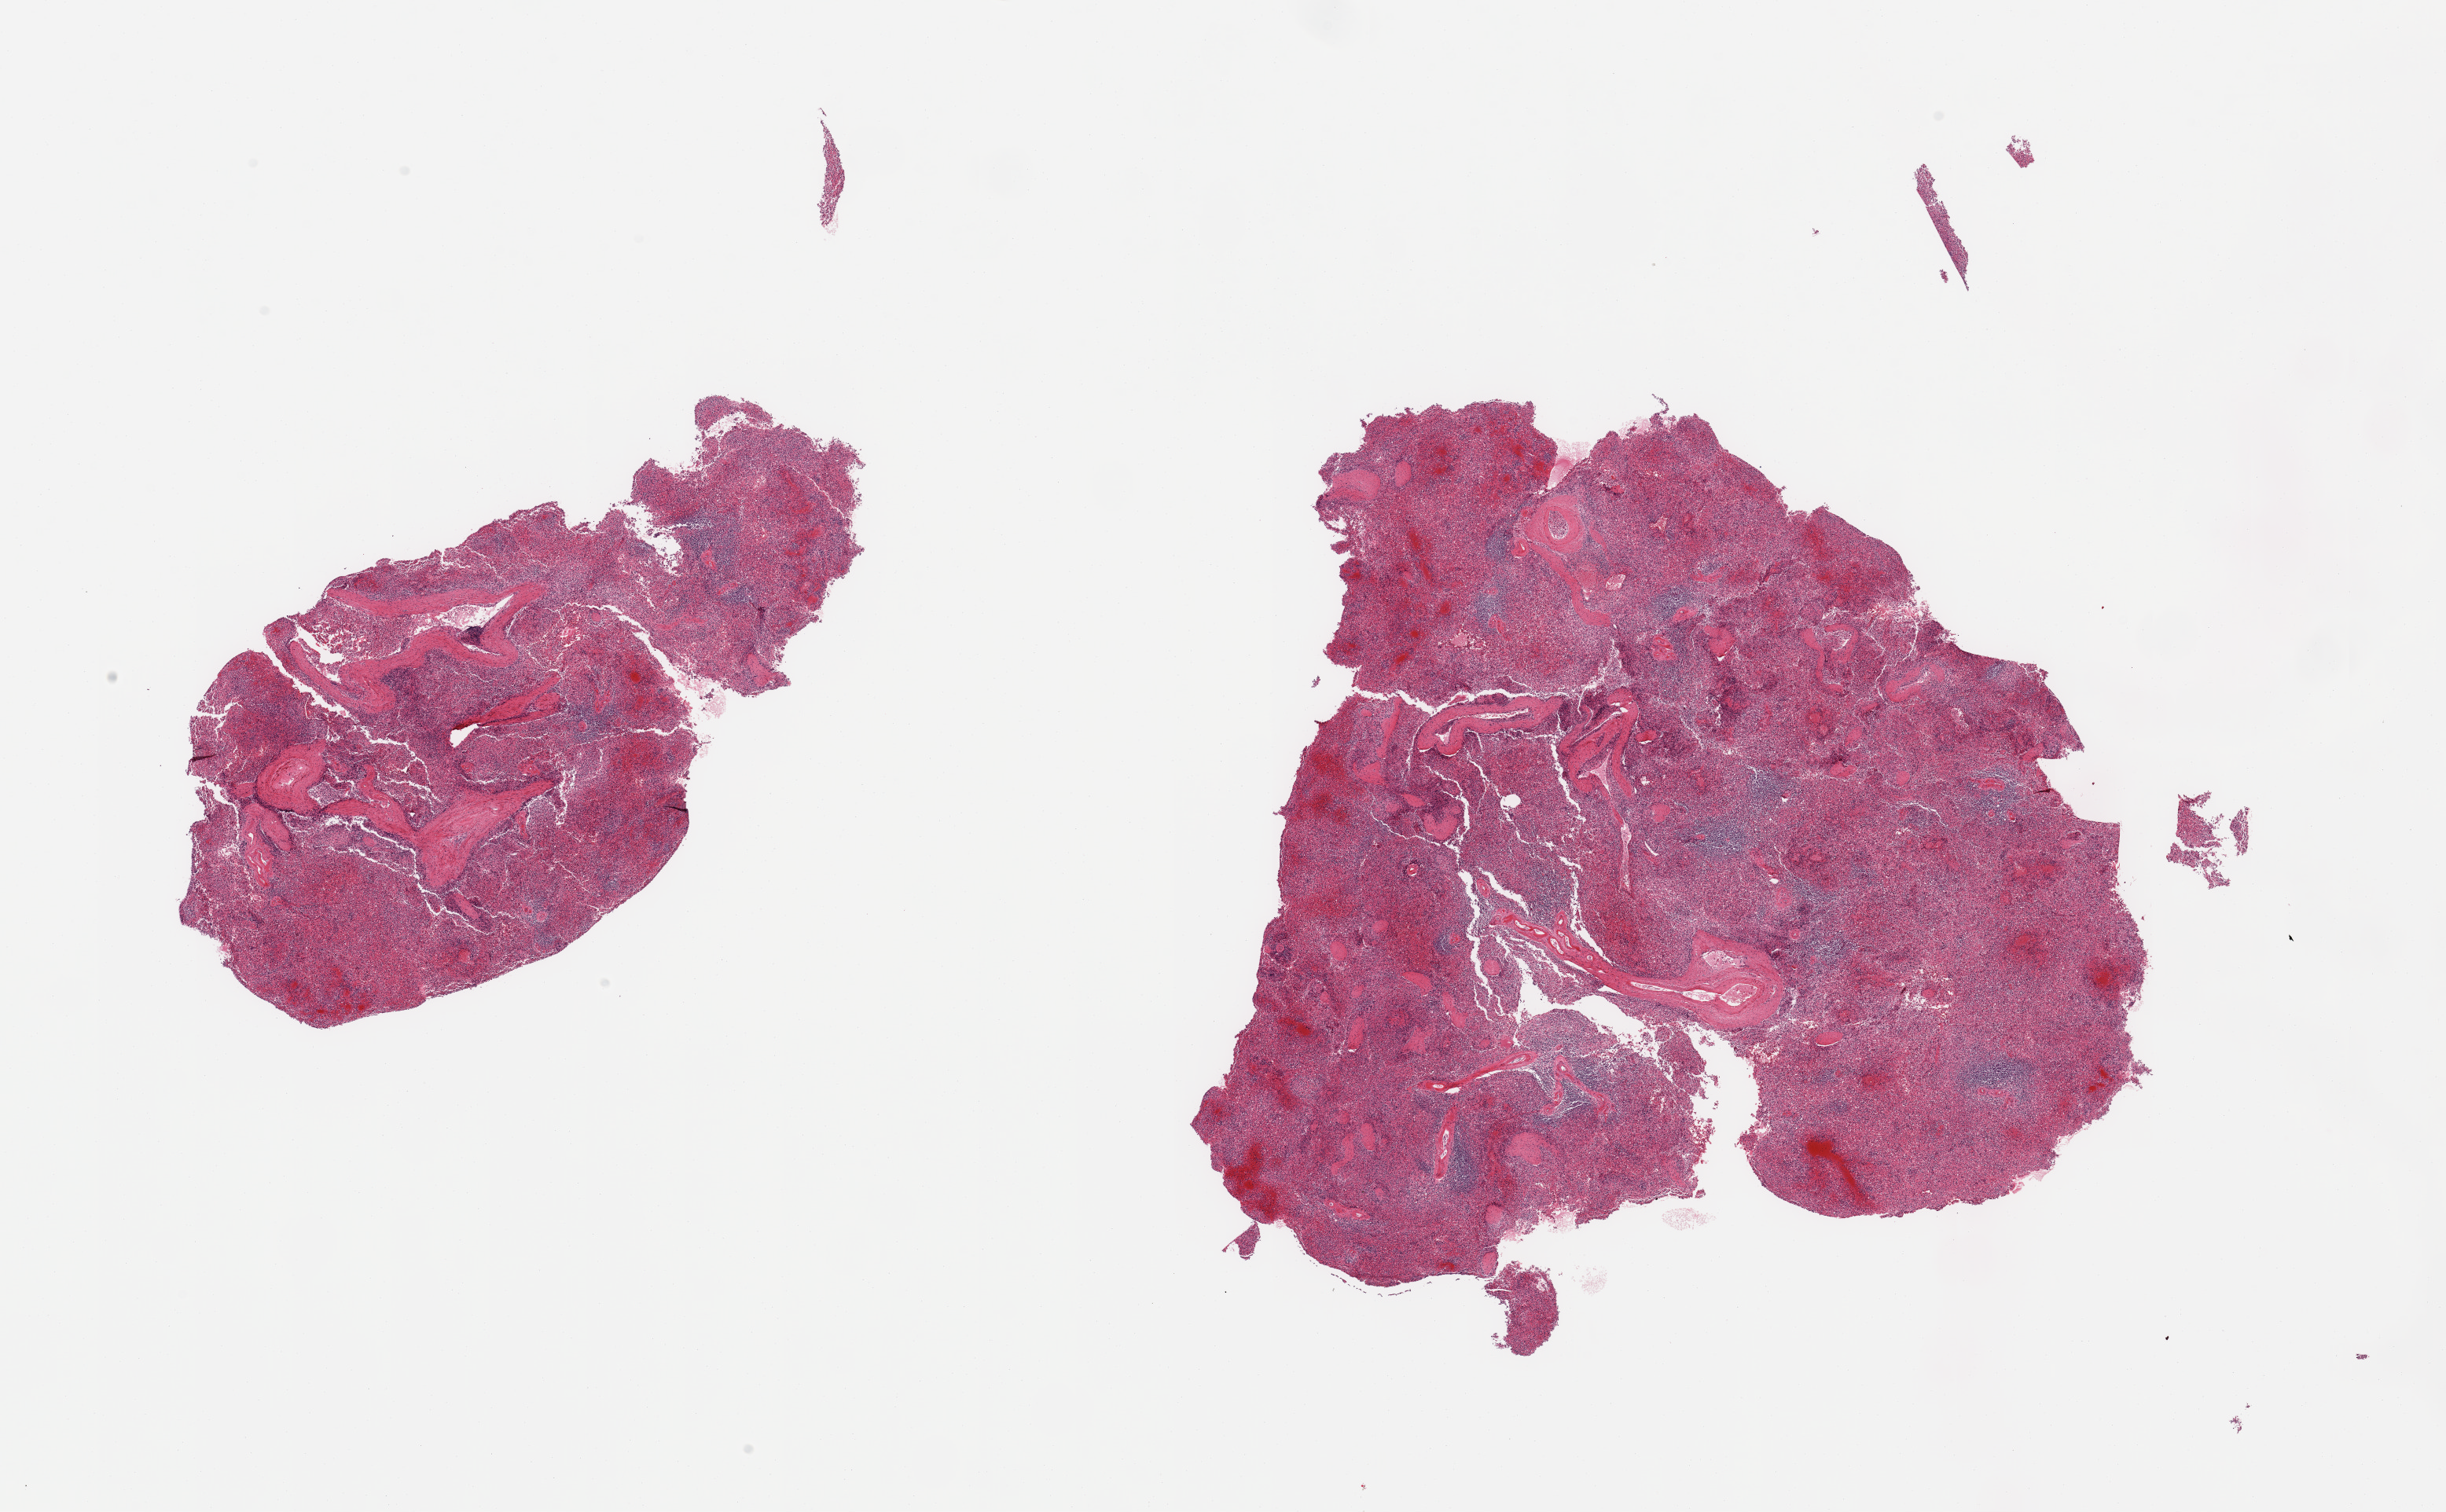
Whole-slide image, H&E stain, brightfield — a low-resolution overview of the entire scanned area, about 24.6 x 15.2 mm; PAXgene-fixed, paraffin-embedded tissue; sampled site (target tissue): spleen; tissue donor sample. Donor: male.
Pathologist's review note for this sample: 2 pieces; partially fragmented.